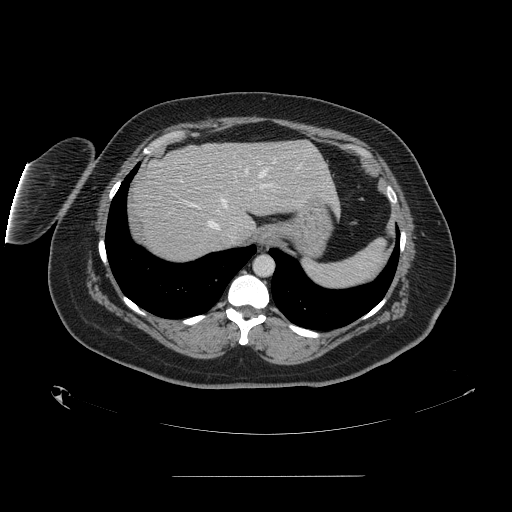
Contrast-enhanced abdominal CT, one axial slice; position 125 of 164 along the scan axis; intravenous contrast given; soft-tissue window (W 400 / L 40 HU); 2.5 mm slice thickness; 512 × 512 image matrix, field of view 495 × 495 mm. Female patient, age 52 years. Case-level facts recorded for this patient, not image findings: diagnosis: colorectal cancer liver metastases, imaged before liver resection; multiple liver metastases: yes; largest metastasis: 3.5 cm; disease in both lobes: no.
Annotated regions visible in this slice (outlined manually by an expert reader):
- hepatic veins: bounding box (x1, y1, x2, y2) in pixels: (207, 169, 267, 238)
- liver: (131, 141, 337, 262)
- planned liver remnant (the part of the liver to remain after resection): (171, 141, 337, 226)
- portal vein (with intrahepatic branches): (179, 180, 271, 189)